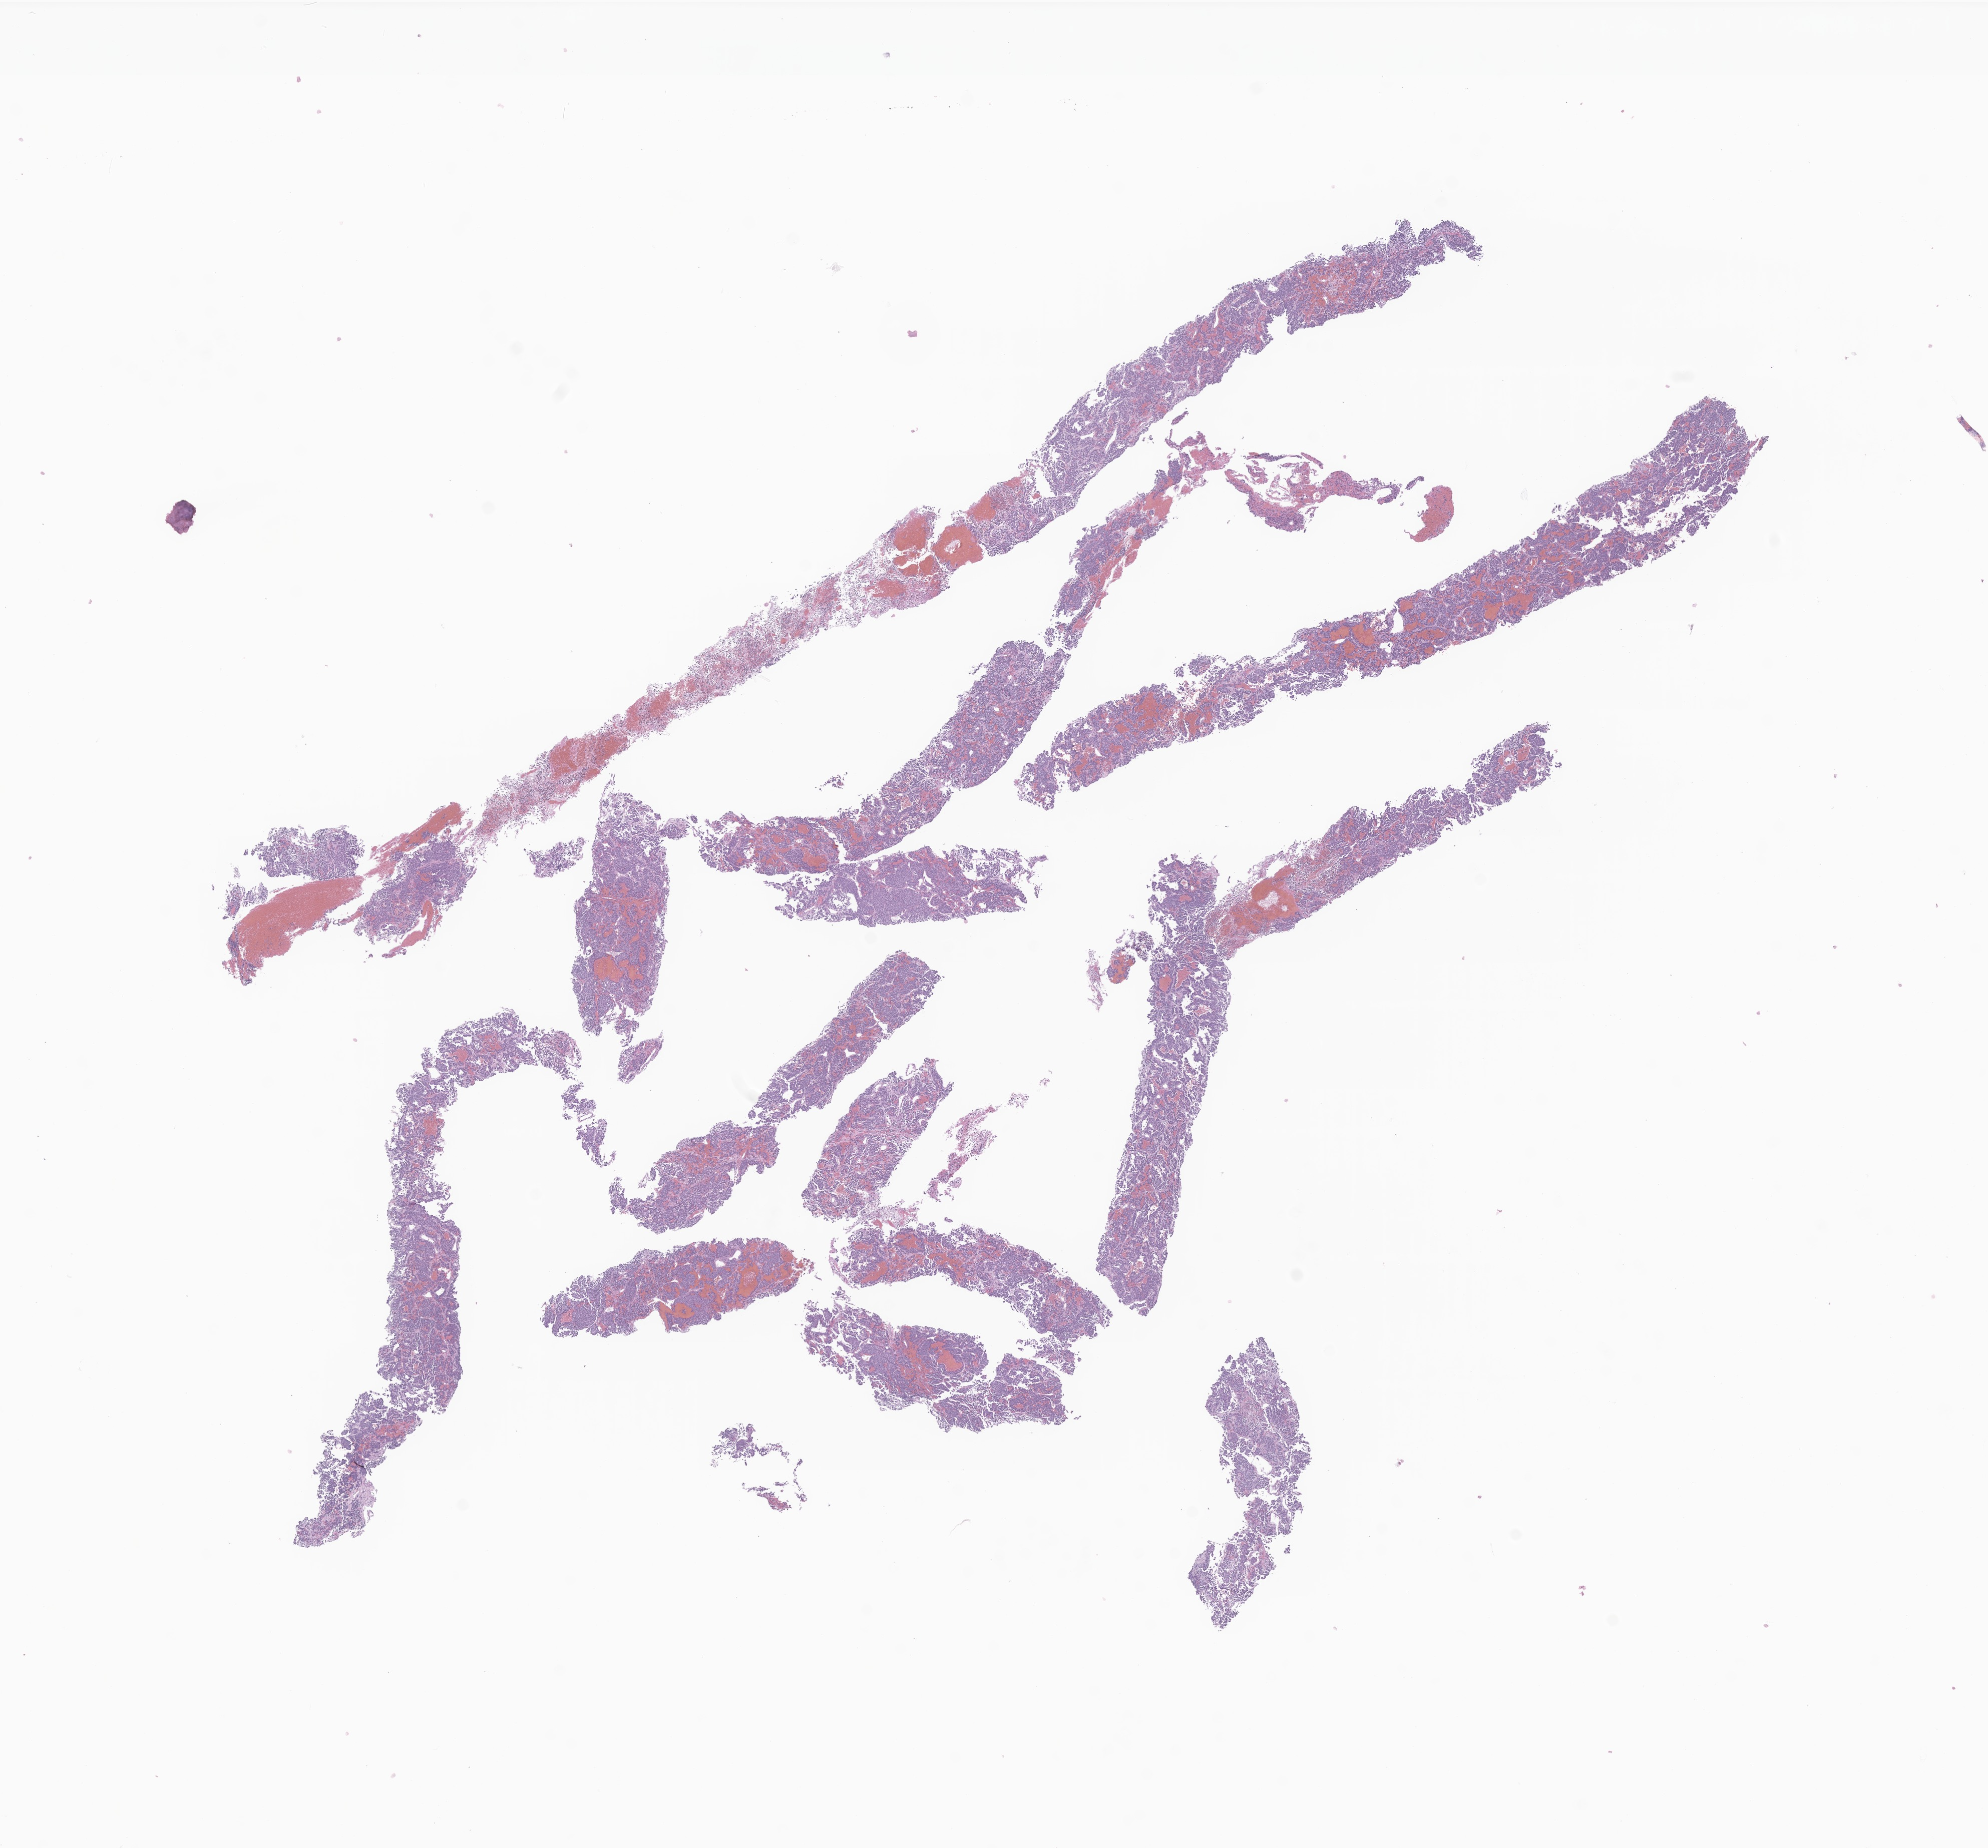
Digitized H&E-stained section of tumor tissue from the adrenal gland, whole scanned area (about 16.7 x 15.6 mm) shown as a low-resolution overview. Formalin-fixed paraffin-embedded section. Female patient, age 63 months.
Diagnosis: Neuroblastoma, NOS.